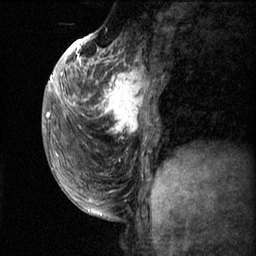
Breast MRI (dynamic contrast-enhanced), one sagittal slice. Position 24 of 60 along the scan axis. Dynamic contrast-enhanced series, image 2 of 3 at this slice position (ordered by acquisition). 1.5 T. TE 4.2 ms, TR 11.1 ms. 2 mm slice thickness. 256 × 256 image matrix. Patient: female, 50 years.
Outlined on this slice (semi-automatically segmented with operator editing):
- analysis volume of interest (the breast-tissue region the enhancement analysis was run in; not a lesion): bounding box [x1, y1, x2, y2] px = [82, 56, 164, 143]
- tumour enhancement mask (voxels above the 70 % enhancement threshold inside the analysis volume of interest): [82, 58, 151, 133]